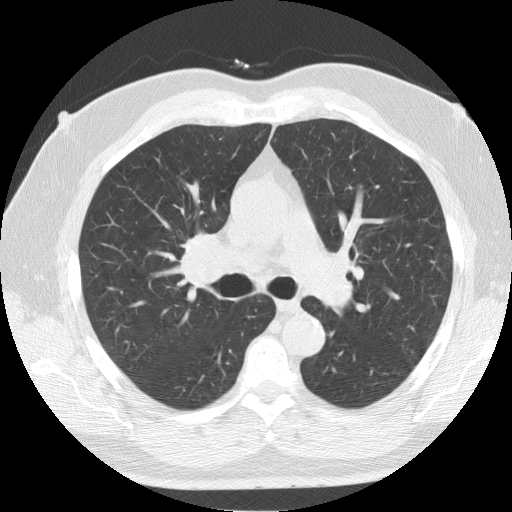
Chest CT (low-dose screening protocol), one axial image; second screening round (one year after baseline); lung window (W 1500 / L -600 HU); slice 50 of 139 in the series; 512 × 512 image matrix, field of view 376 × 376 mm. Male participant, aged 64 years at enrolment. Former smoker at enrolment.
Expert reader's lesion annotation, bounding box <168,223,257,303> (left, top, right, bottom; pixels). The exam's reader record, not a measurement of the box and not confirmed to be the same lesion: non-calcified nodule or mass ≥4 mm, right lower lobe, 7 × 5 mm, smooth margins, soft tissue attenuation, pre-existing on the prior screen: yes; interval growth: no. Official screen result: positive, other. Participant outcome: lung cancer diagnosed 63 days after this screen — adenocarcinoma, NOS, right upper lobe, poorly differentiated (G3), stage IB (AJCC 6th edition), 37 mm at pathology.